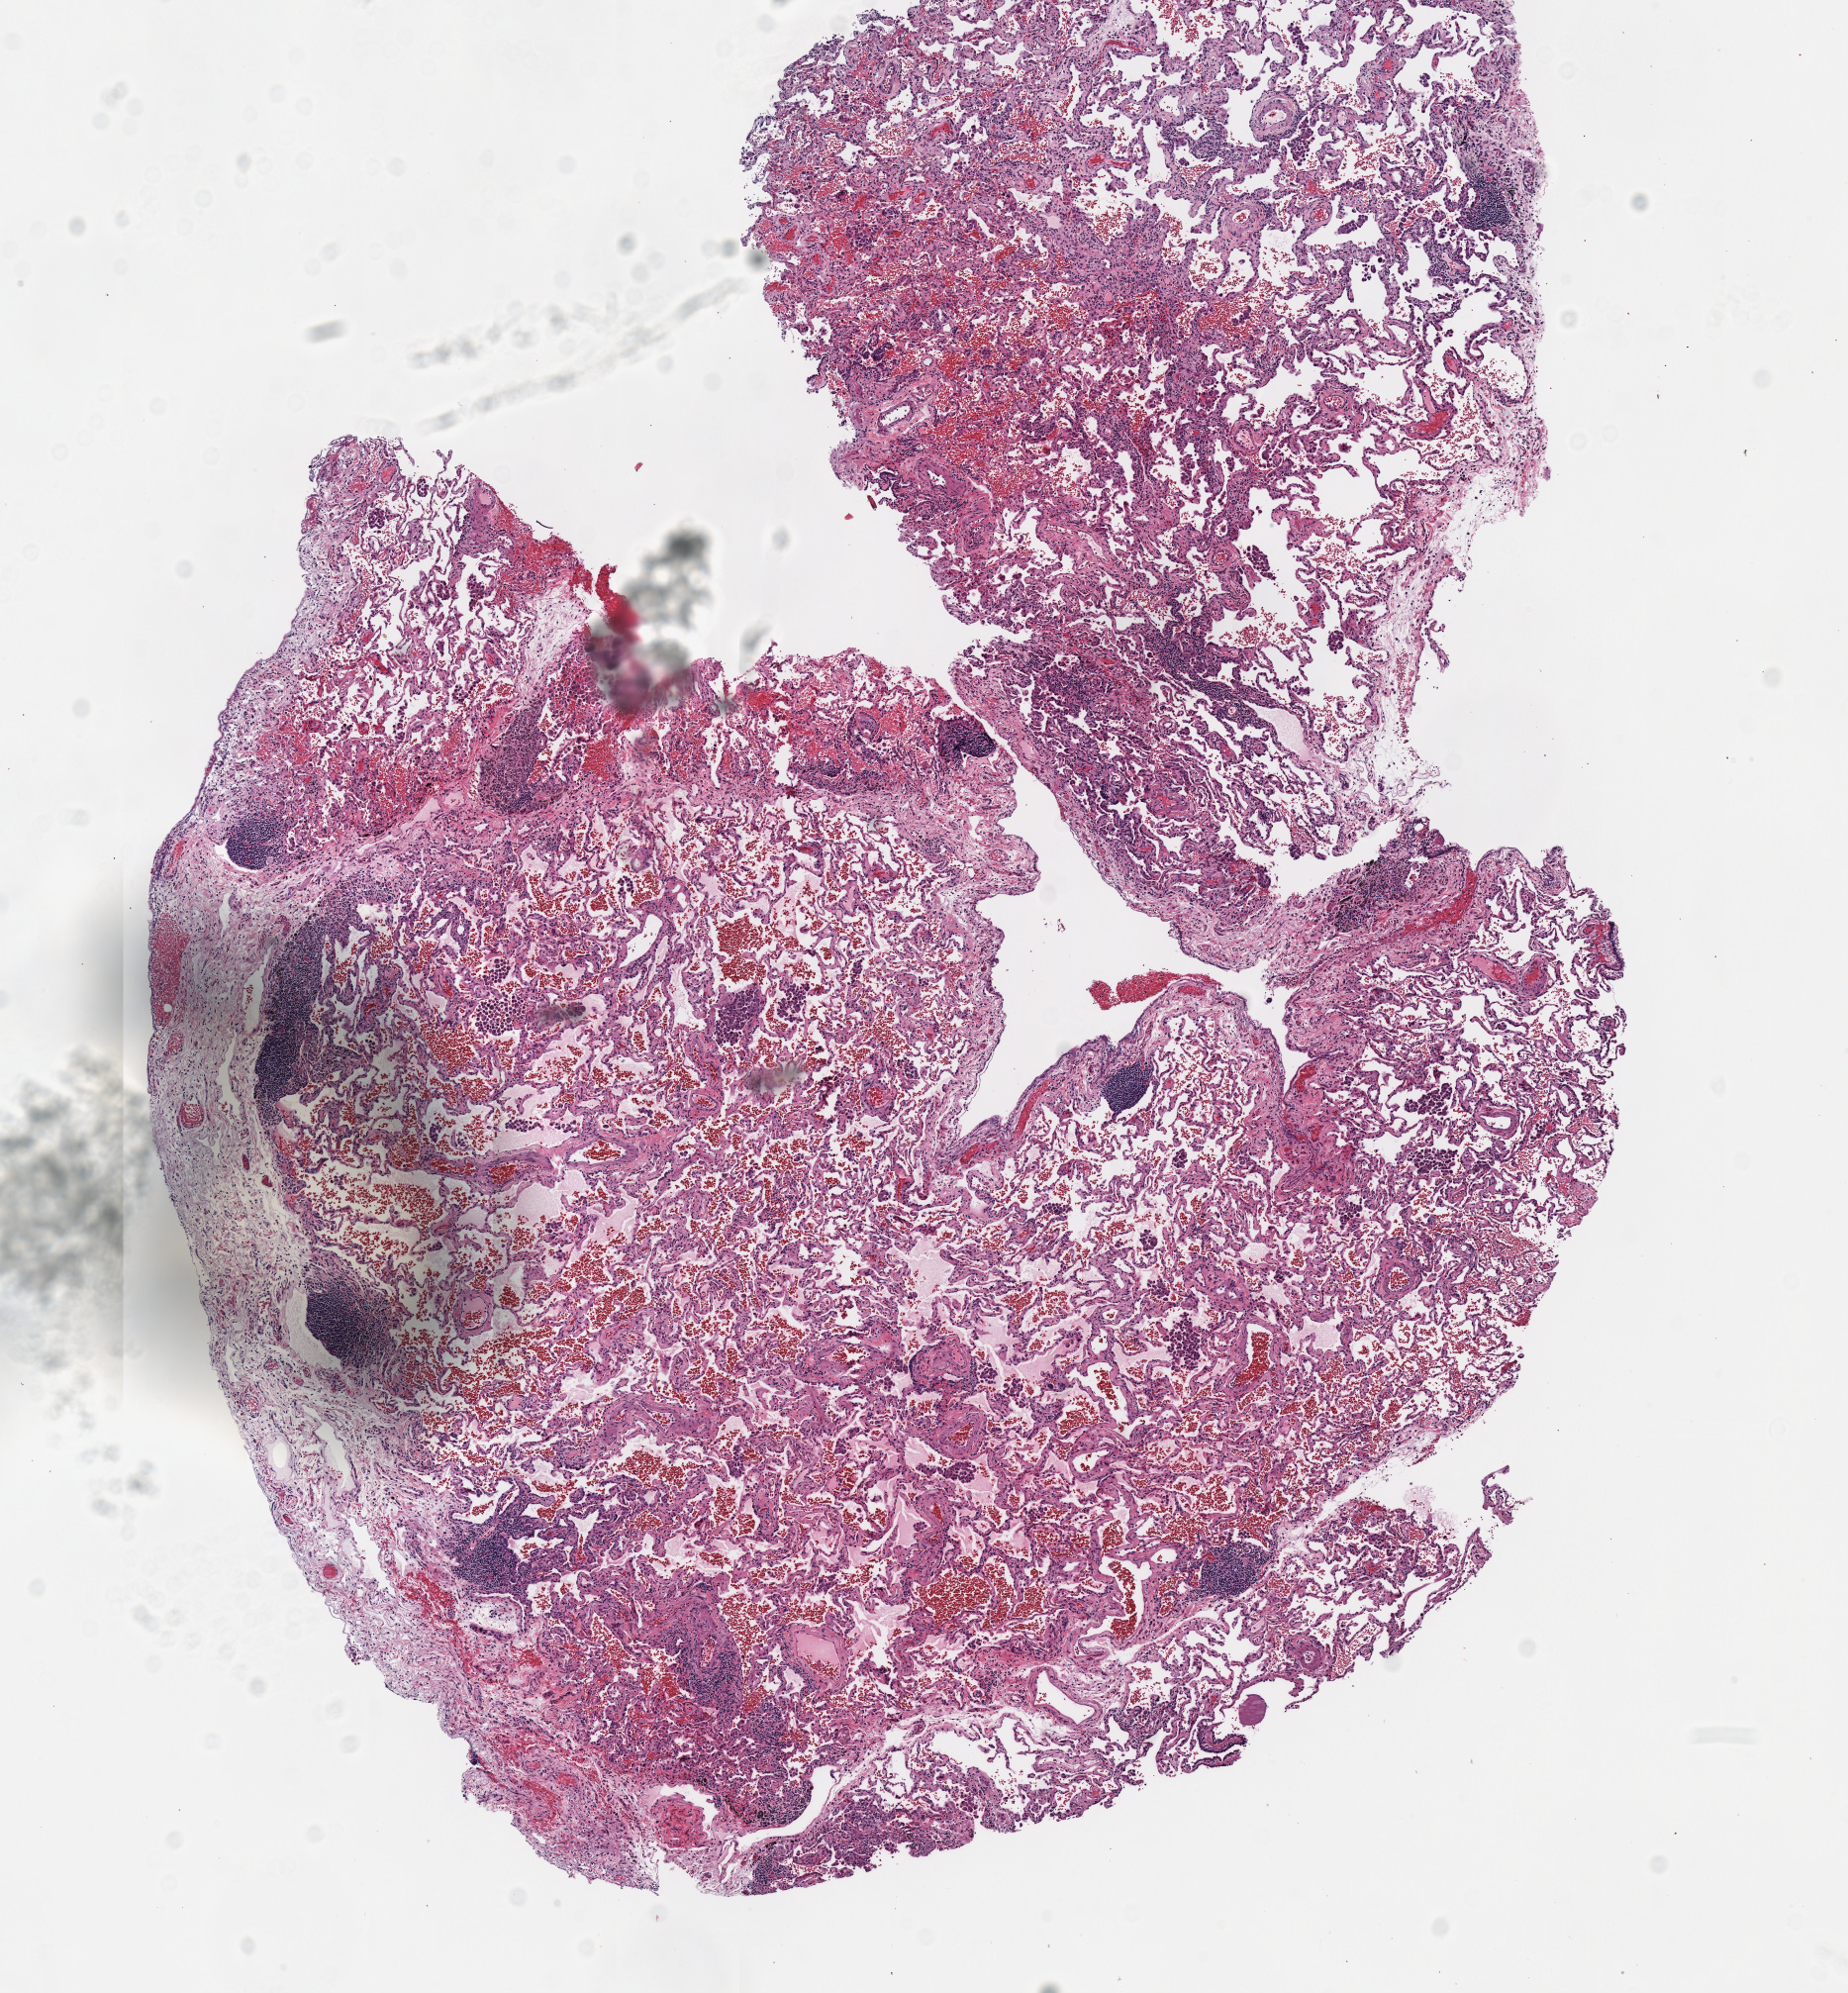
Hematoxylin and eosin (H&E) stained whole-slide image — low-resolution overview of the scanned area, about 7.3 x 7.9 mm. Frozen section. Lung, solid tissue normal (non-tumour tissue) sample. Patient: female, age at initial diagnosis 47 years.
• this section: solid tissue normal sample (biorepository sample class)
• patient diagnosis: Adenocarcinoma, NOS (upper lobe, lung)